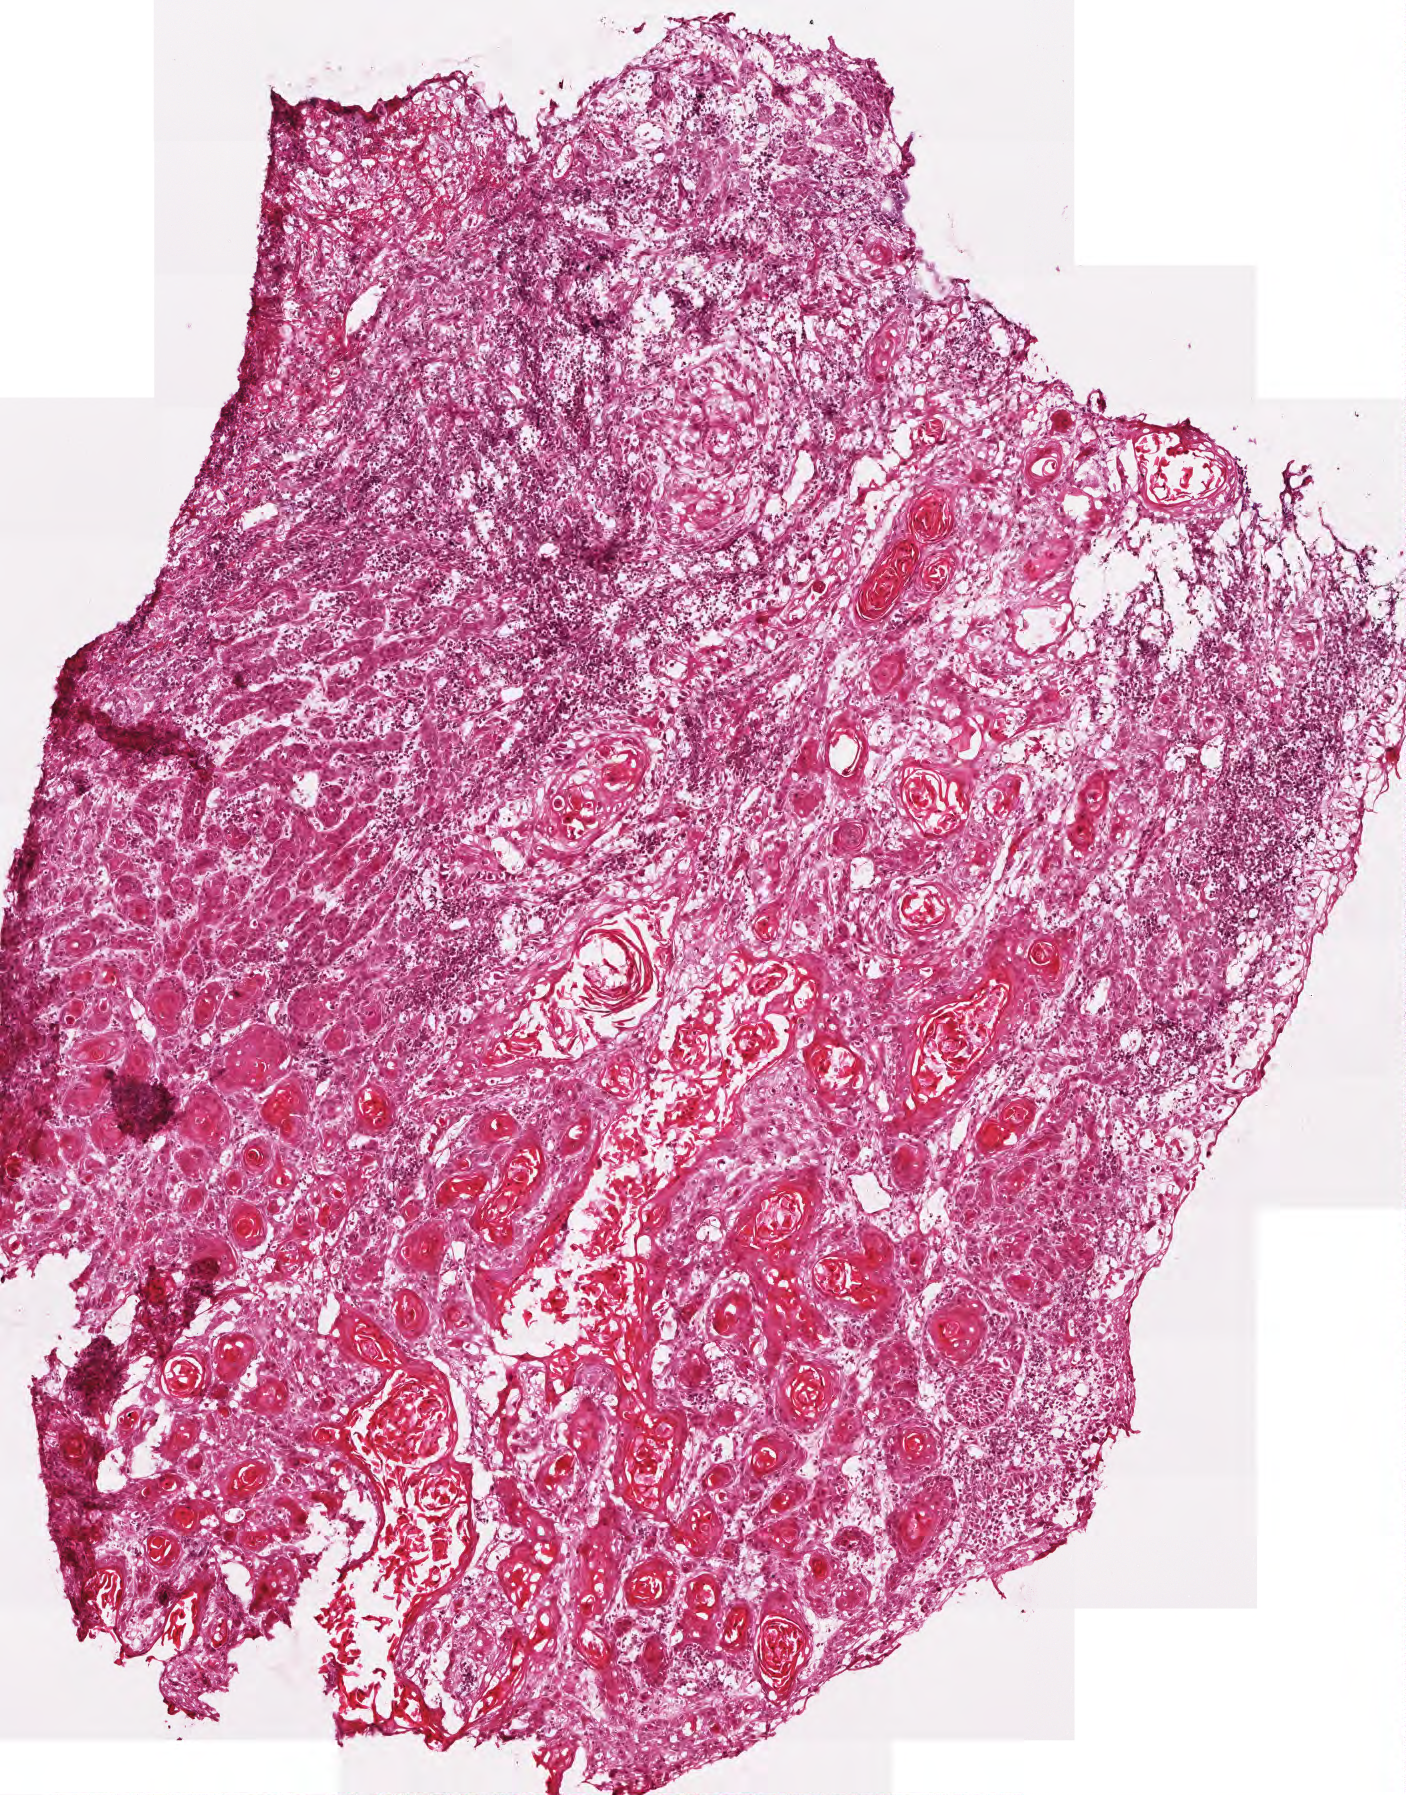
Whole-slide histology image, H&E-stained — a low-resolution overview of the entire scanned area, about 2.8 x 3.6 mm; frozen section; primary tumour sample from the head and neck. Patient: female, age at initial diagnosis 67 years. Histologic grade: G1 (well differentiated). Pathologist review of this section (percent, as recorded): tumour cells 100%, tumour nuclei 60%, normal cells 0%, stromal cells 0%, necrosis 0%. Infiltration values recorded for this section: lymphocyte infiltration 30%, monocyte infiltration 0%, neutrophil infiltration 0%.
AJCC pathologic stage: IVA (6th edition). Diagnosis: Squamous cell carcinoma, NOS (tongue, NOS).